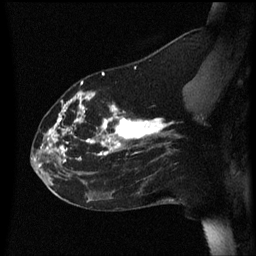
Breast MRI (dynamic contrast-enhanced), one sagittal slice; dynamic contrast-enhanced series, image 2 of 3 at this slice position (ordered by acquisition); 1.5 T; TE 4.2 ms, TR 8.4 ms; 2.2 mm slice thickness; 256 × 256 image matrix, field of view 200 × 200 mm. Female patient, age 35 years. From the clinical record (not read from this slice): setting: breast cancer imaged before/during neoadjuvant chemotherapy; receptor status: HER2-positive.
Outlined on this slice (semi-automatically segmented with operator editing):
- analysis volume of interest (the breast-tissue region the enhancement analysis was run in; not a lesion): bounding box <31,72,178,173> (left, top, right, bottom; pixels)
- tumour enhancement mask (voxels above the 70 % enhancement threshold inside the analysis volume of interest): <40,72,174,167>